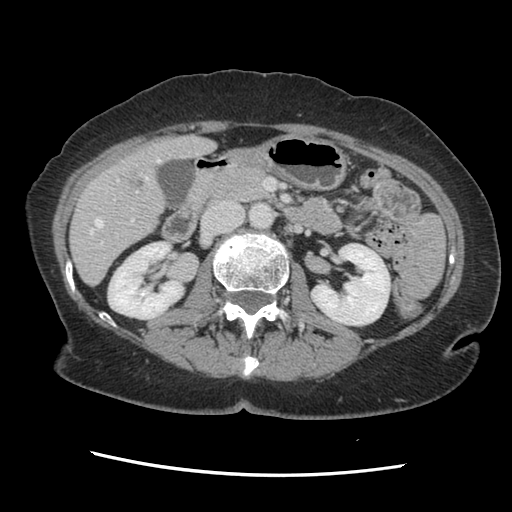
Contrast-enhanced abdominal CT, one axial slice; soft-tissue window (W 400 / L 40 HU); 2.5 mm slice thickness; 512 × 512 image matrix, field of view 330 × 330 mm. Female patient, age 61 years. From the clinical record (not read from this slice): diagnosis: colorectal cancer liver metastases, imaged before liver resection; multiple liver metastases: no; largest metastasis: 2.4 cm; chemotherapy before resection: no.
Outlined on this slice (manually delineated by an expert):
- hepatic veins: bounding box <90,159,161,235> (left, top, right, bottom; pixels)
- liver: <71,137,213,284>
- planned liver remnant (the part of the liver to remain after resection): <71,140,212,284>
- portal vein (with intrahepatic branches): <101,180,138,244>
- liver metastasis: <125,170,145,191>